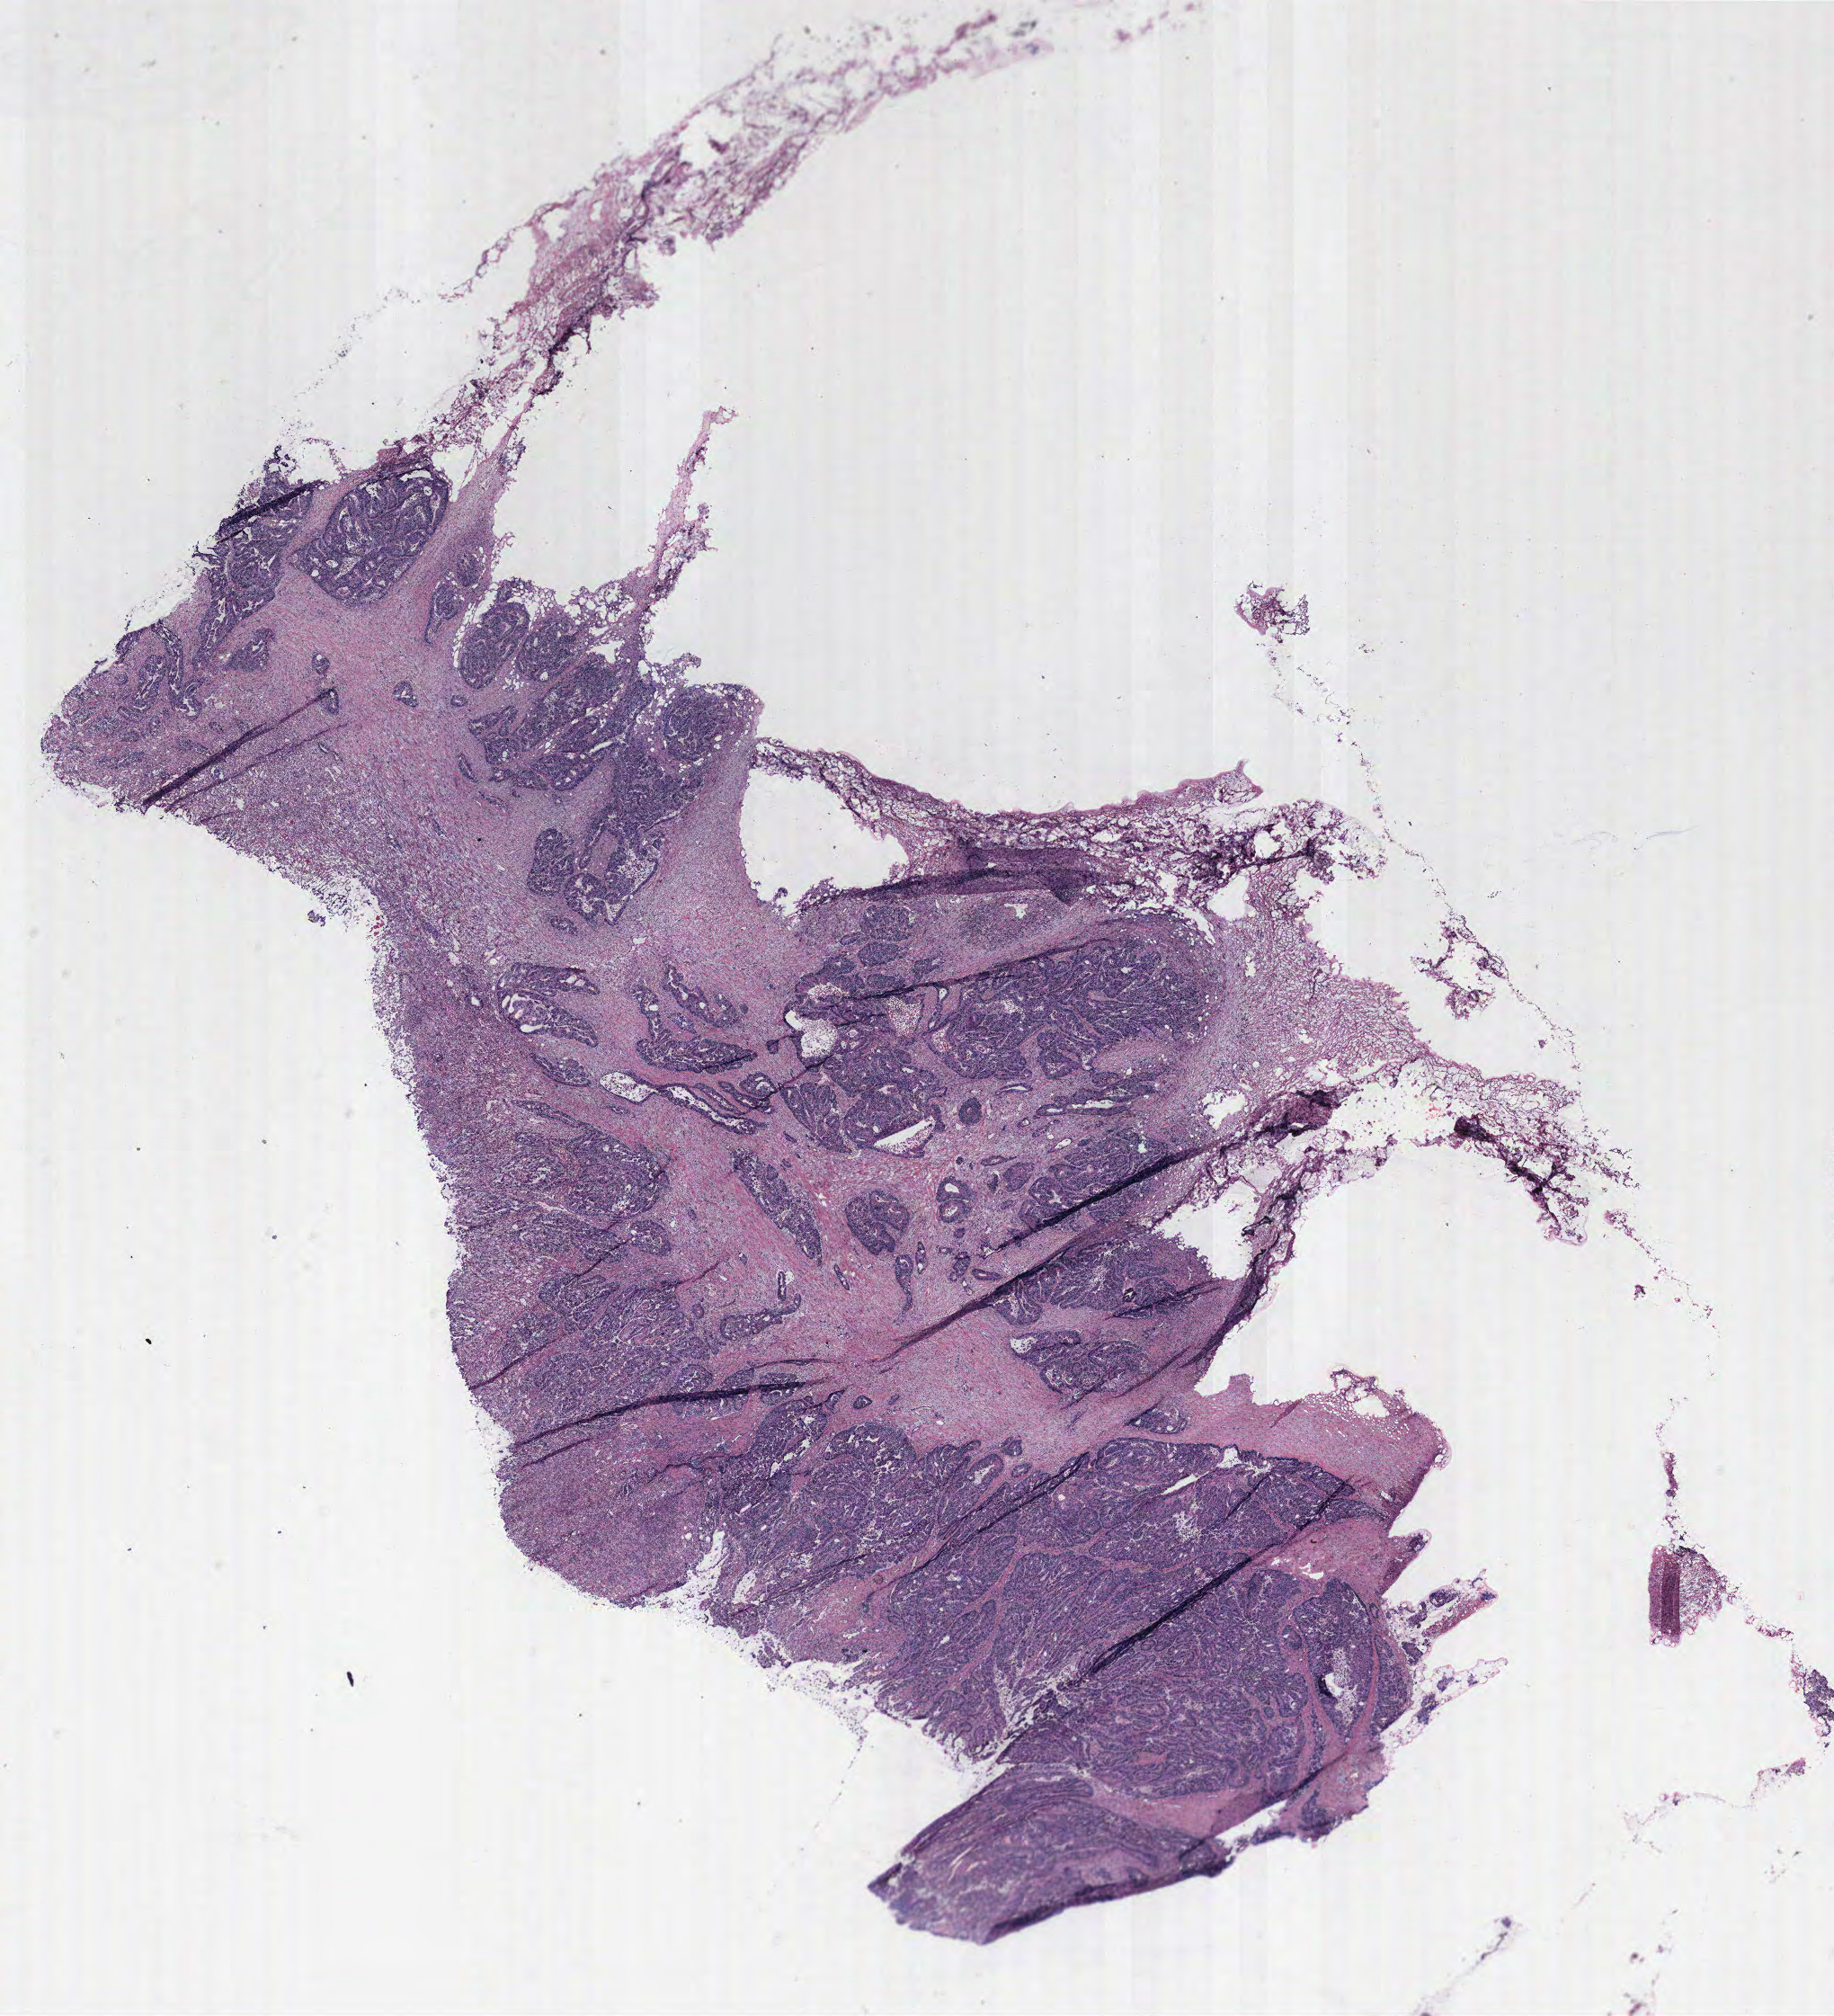
H&E whole-slide image, shown as a low-resolution overview of the whole scanned area (about 16.3 x 17.9 mm, from a 40x scan), colon, tumour tissue. 67-year-old female patient.
Diagnosis: Adenocarcinoma, NOS. Primary tumour site (as recorded): colon. AJCC pathologic stage: IIA.